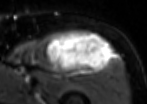
MRI of an extremity soft-tissue mass, one axial slice; slice 67 of 85 in the series (ordered by position); T2-weighted fat-saturated; MR volume resampled by the dataset authors to the PET/CT grid (not the native acquisition matrix); 3.27 mm slice thickness; 147 × 104 image matrix. Male patient. From the clinical record (not read from this slice): histological type: extraskeletal osteosarcoma; grade: high; site of the primary tumour: thigh.
Outlined on this slice (expert contour drawn on MRI and transferred to this co-registered scan by the dataset authors):
- gross tumour volume (mass): bounding box <44,33,112,72> (left, top, right, bottom; pixels)